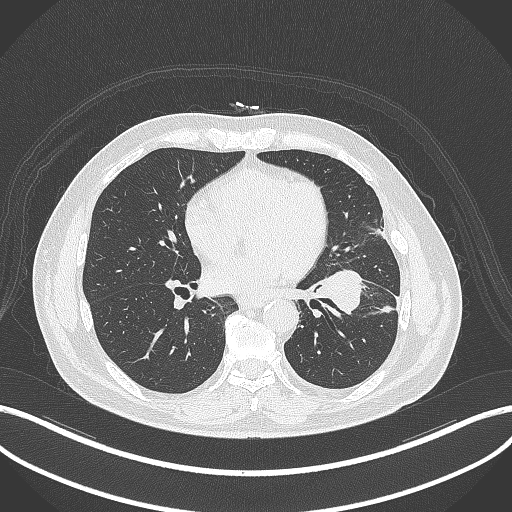
Chest CT, one axial slice. Slice 158 of 230 in the series (ordered by position). Lung window (W 1500 / L -600 HU). 512 × 512 image matrix. Patient: male, 68 years. From the clinical record (not read from this slice): clinical TNM (as recorded): T2b N0 M0.
Structures marked on this image (bounding box drawn by a radiologist):
- lung tumour (recorded histology: squamous cell carcinoma): bounding box [x1, y1, x2, y2] px = [312, 268, 365, 316]